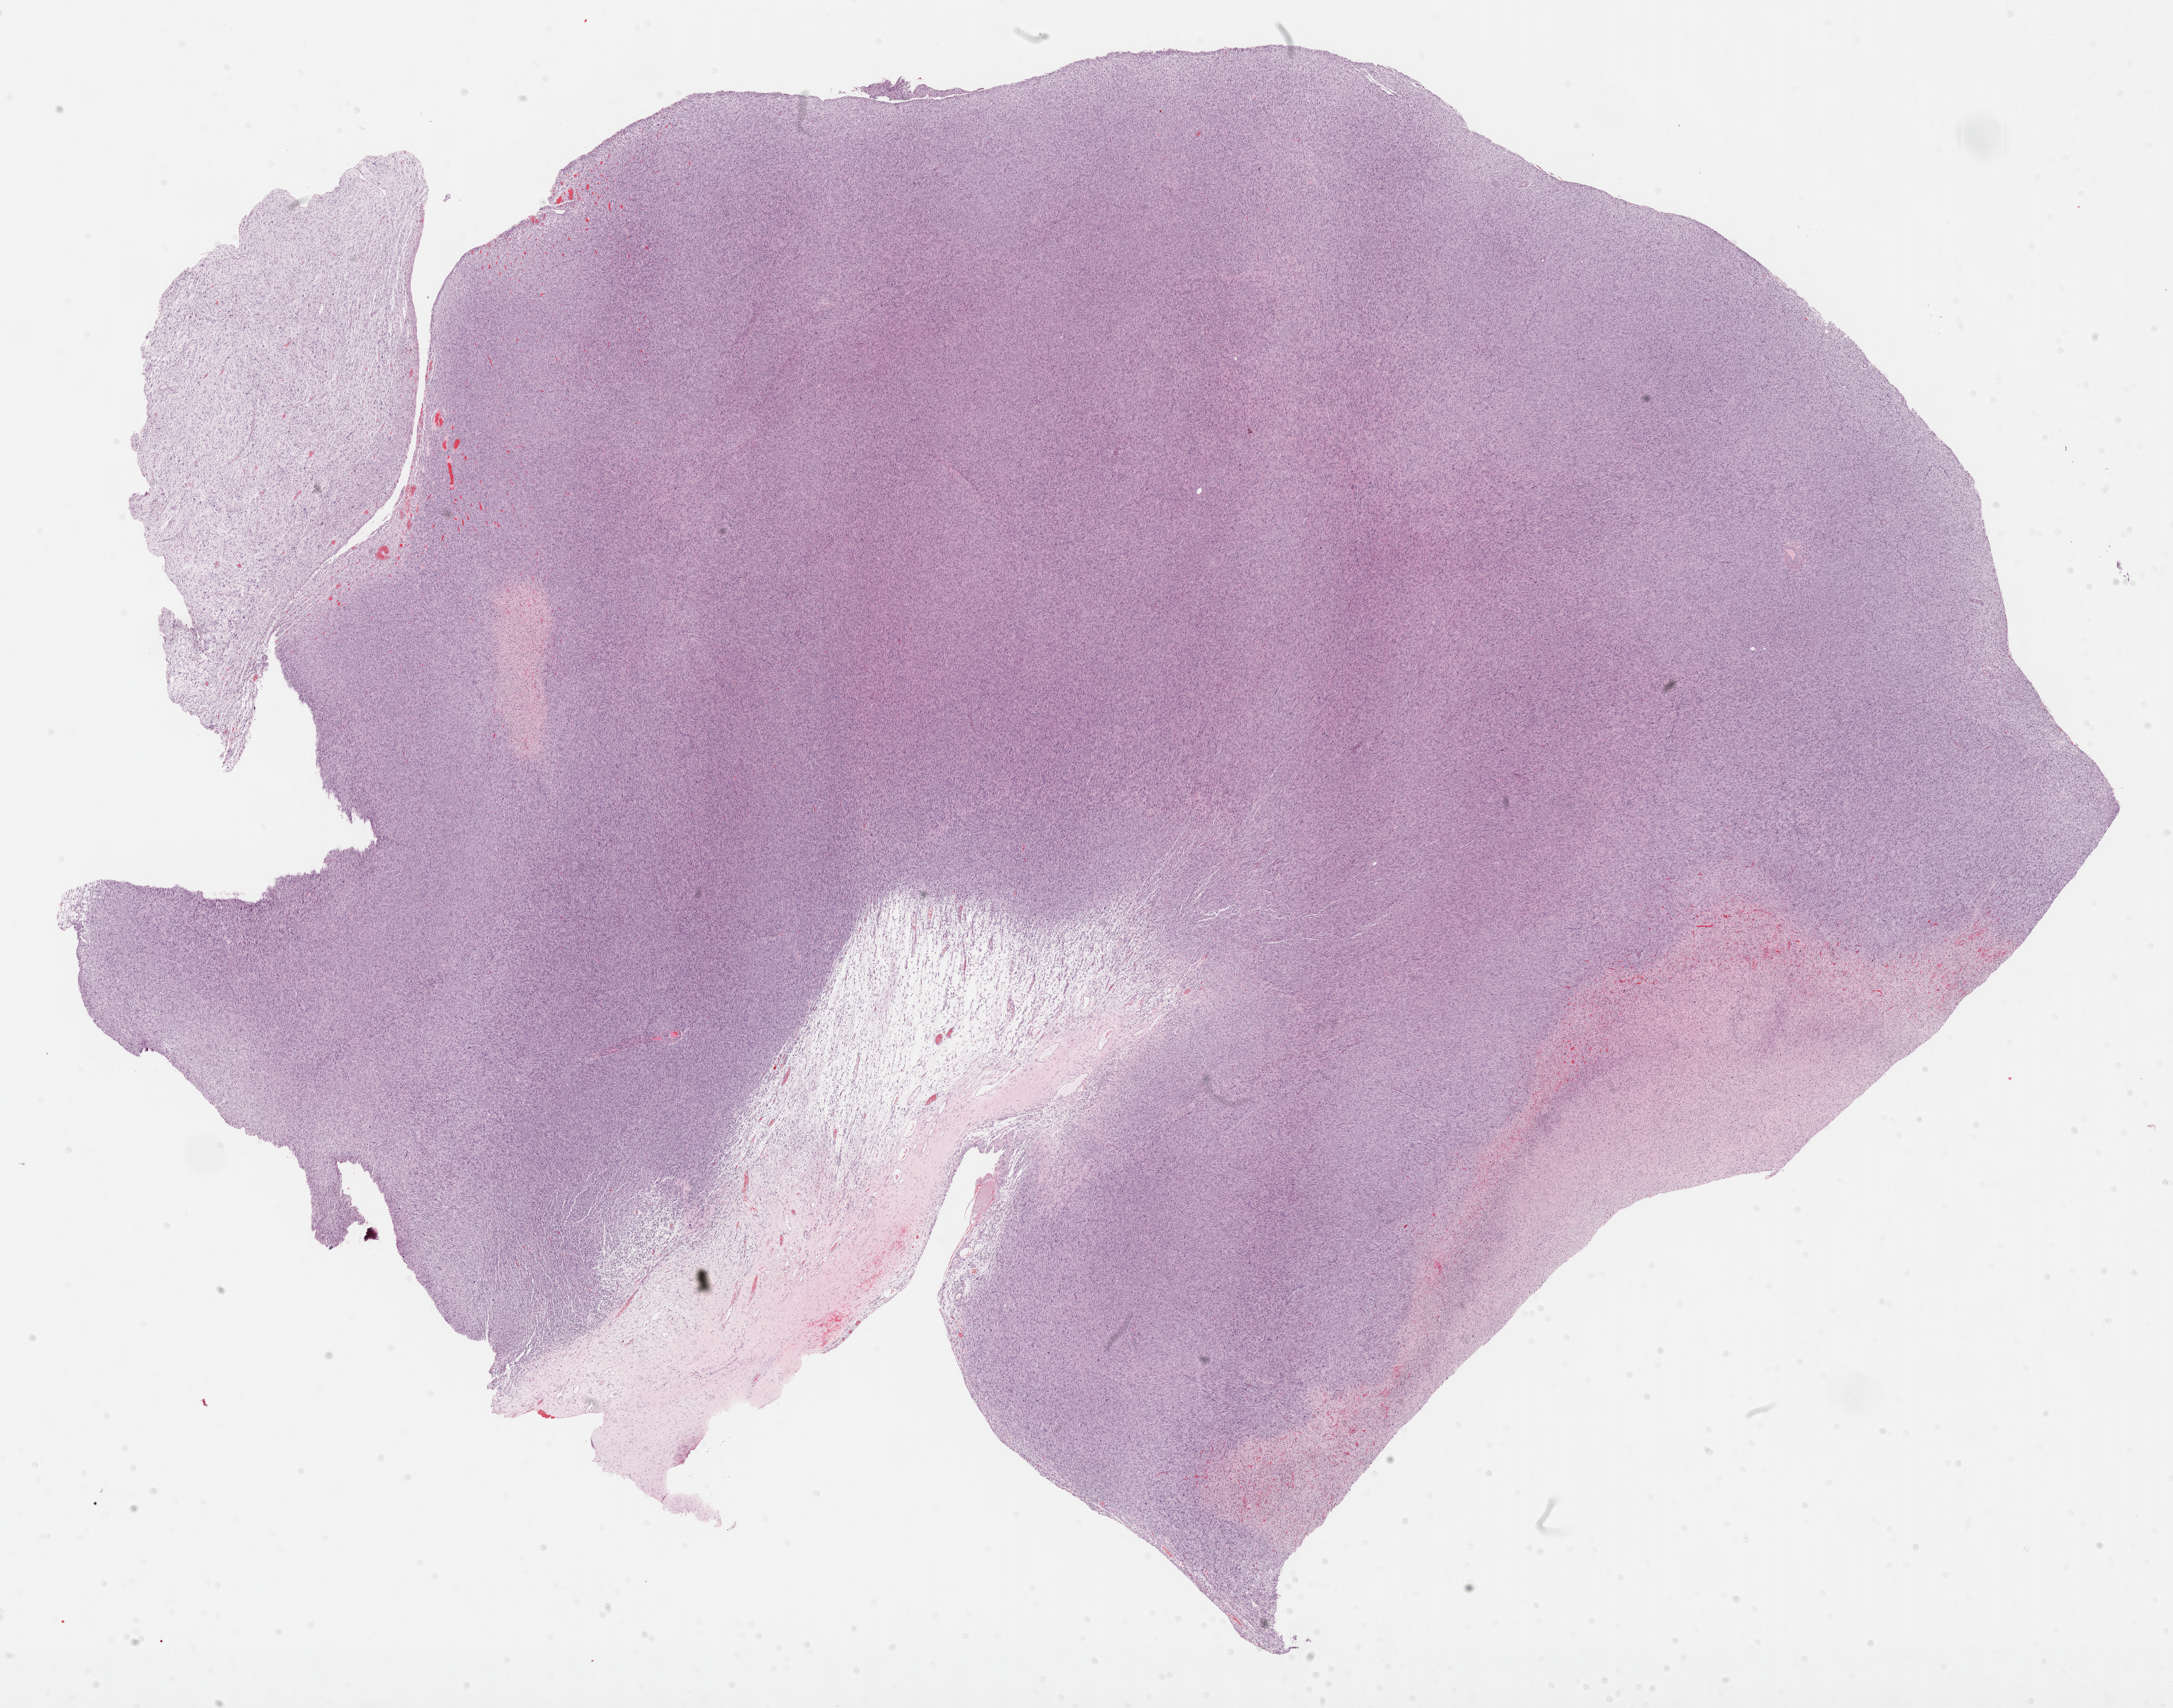
Hematoxylin and eosin (H&E) stained whole-slide image — shown as a low-resolution overview of the whole scanned area (about 25.7 x 20.2 mm, slide scanned at 40x); formalin-fixed paraffin-embedded (FFPE) diagnostic section; primary tumour sample from the connective, subcutaneous and other soft tissues. Female patient; age at initial diagnosis 63 years.
Histologic diagnosis: Malignant fibrous histiocytoma.